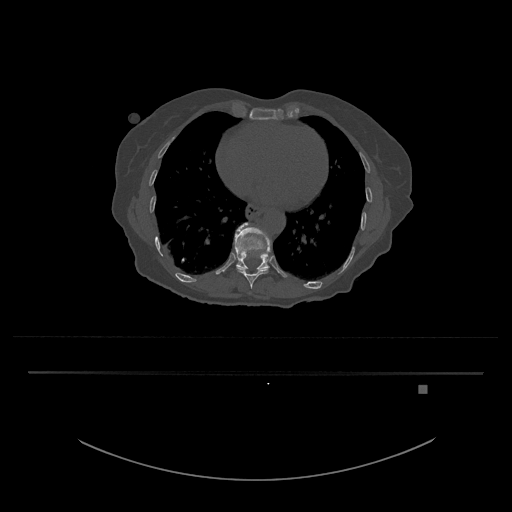
CT including the spine, one axial slice; slice 693 of 797 in the series (ordered by position); 120 kVp; bone window (W 1800 / L 400 HU); 512 × 512 image matrix. Patient: female, 57 years. Case-level facts recorded for this patient, not image findings: primary cancer: cervical.
Annotated regions visible in this slice (semi-automatically segmented with operator editing):
- T10 vertebra: bounding box (x1, y1, x2, y2) in pixels: (237, 268, 268, 289)
- T11 vertebra: (234, 223, 272, 270)